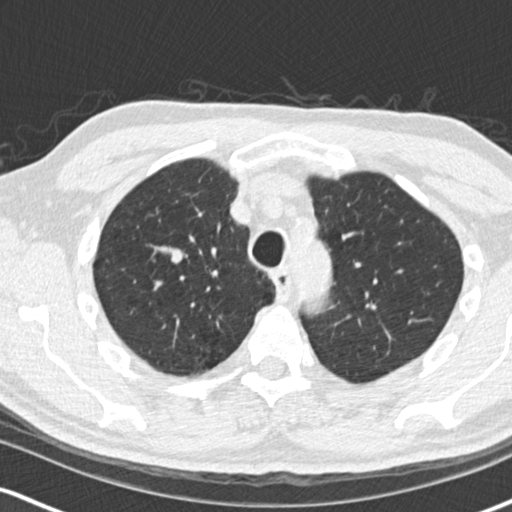
Low-dose screening chest CT, one axial slice; position 120 of 170 along the scan axis; lung window (W 1500 / L -600 HU); 512 × 512 image matrix, field of view 320 × 320 mm.
Structures marked on this image (expert manual segmentation):
- lesion 1 (tumor, upper lobe of right lung): bounding box (x1, y1, x2, y2) in pixels: (171, 249, 184, 264)